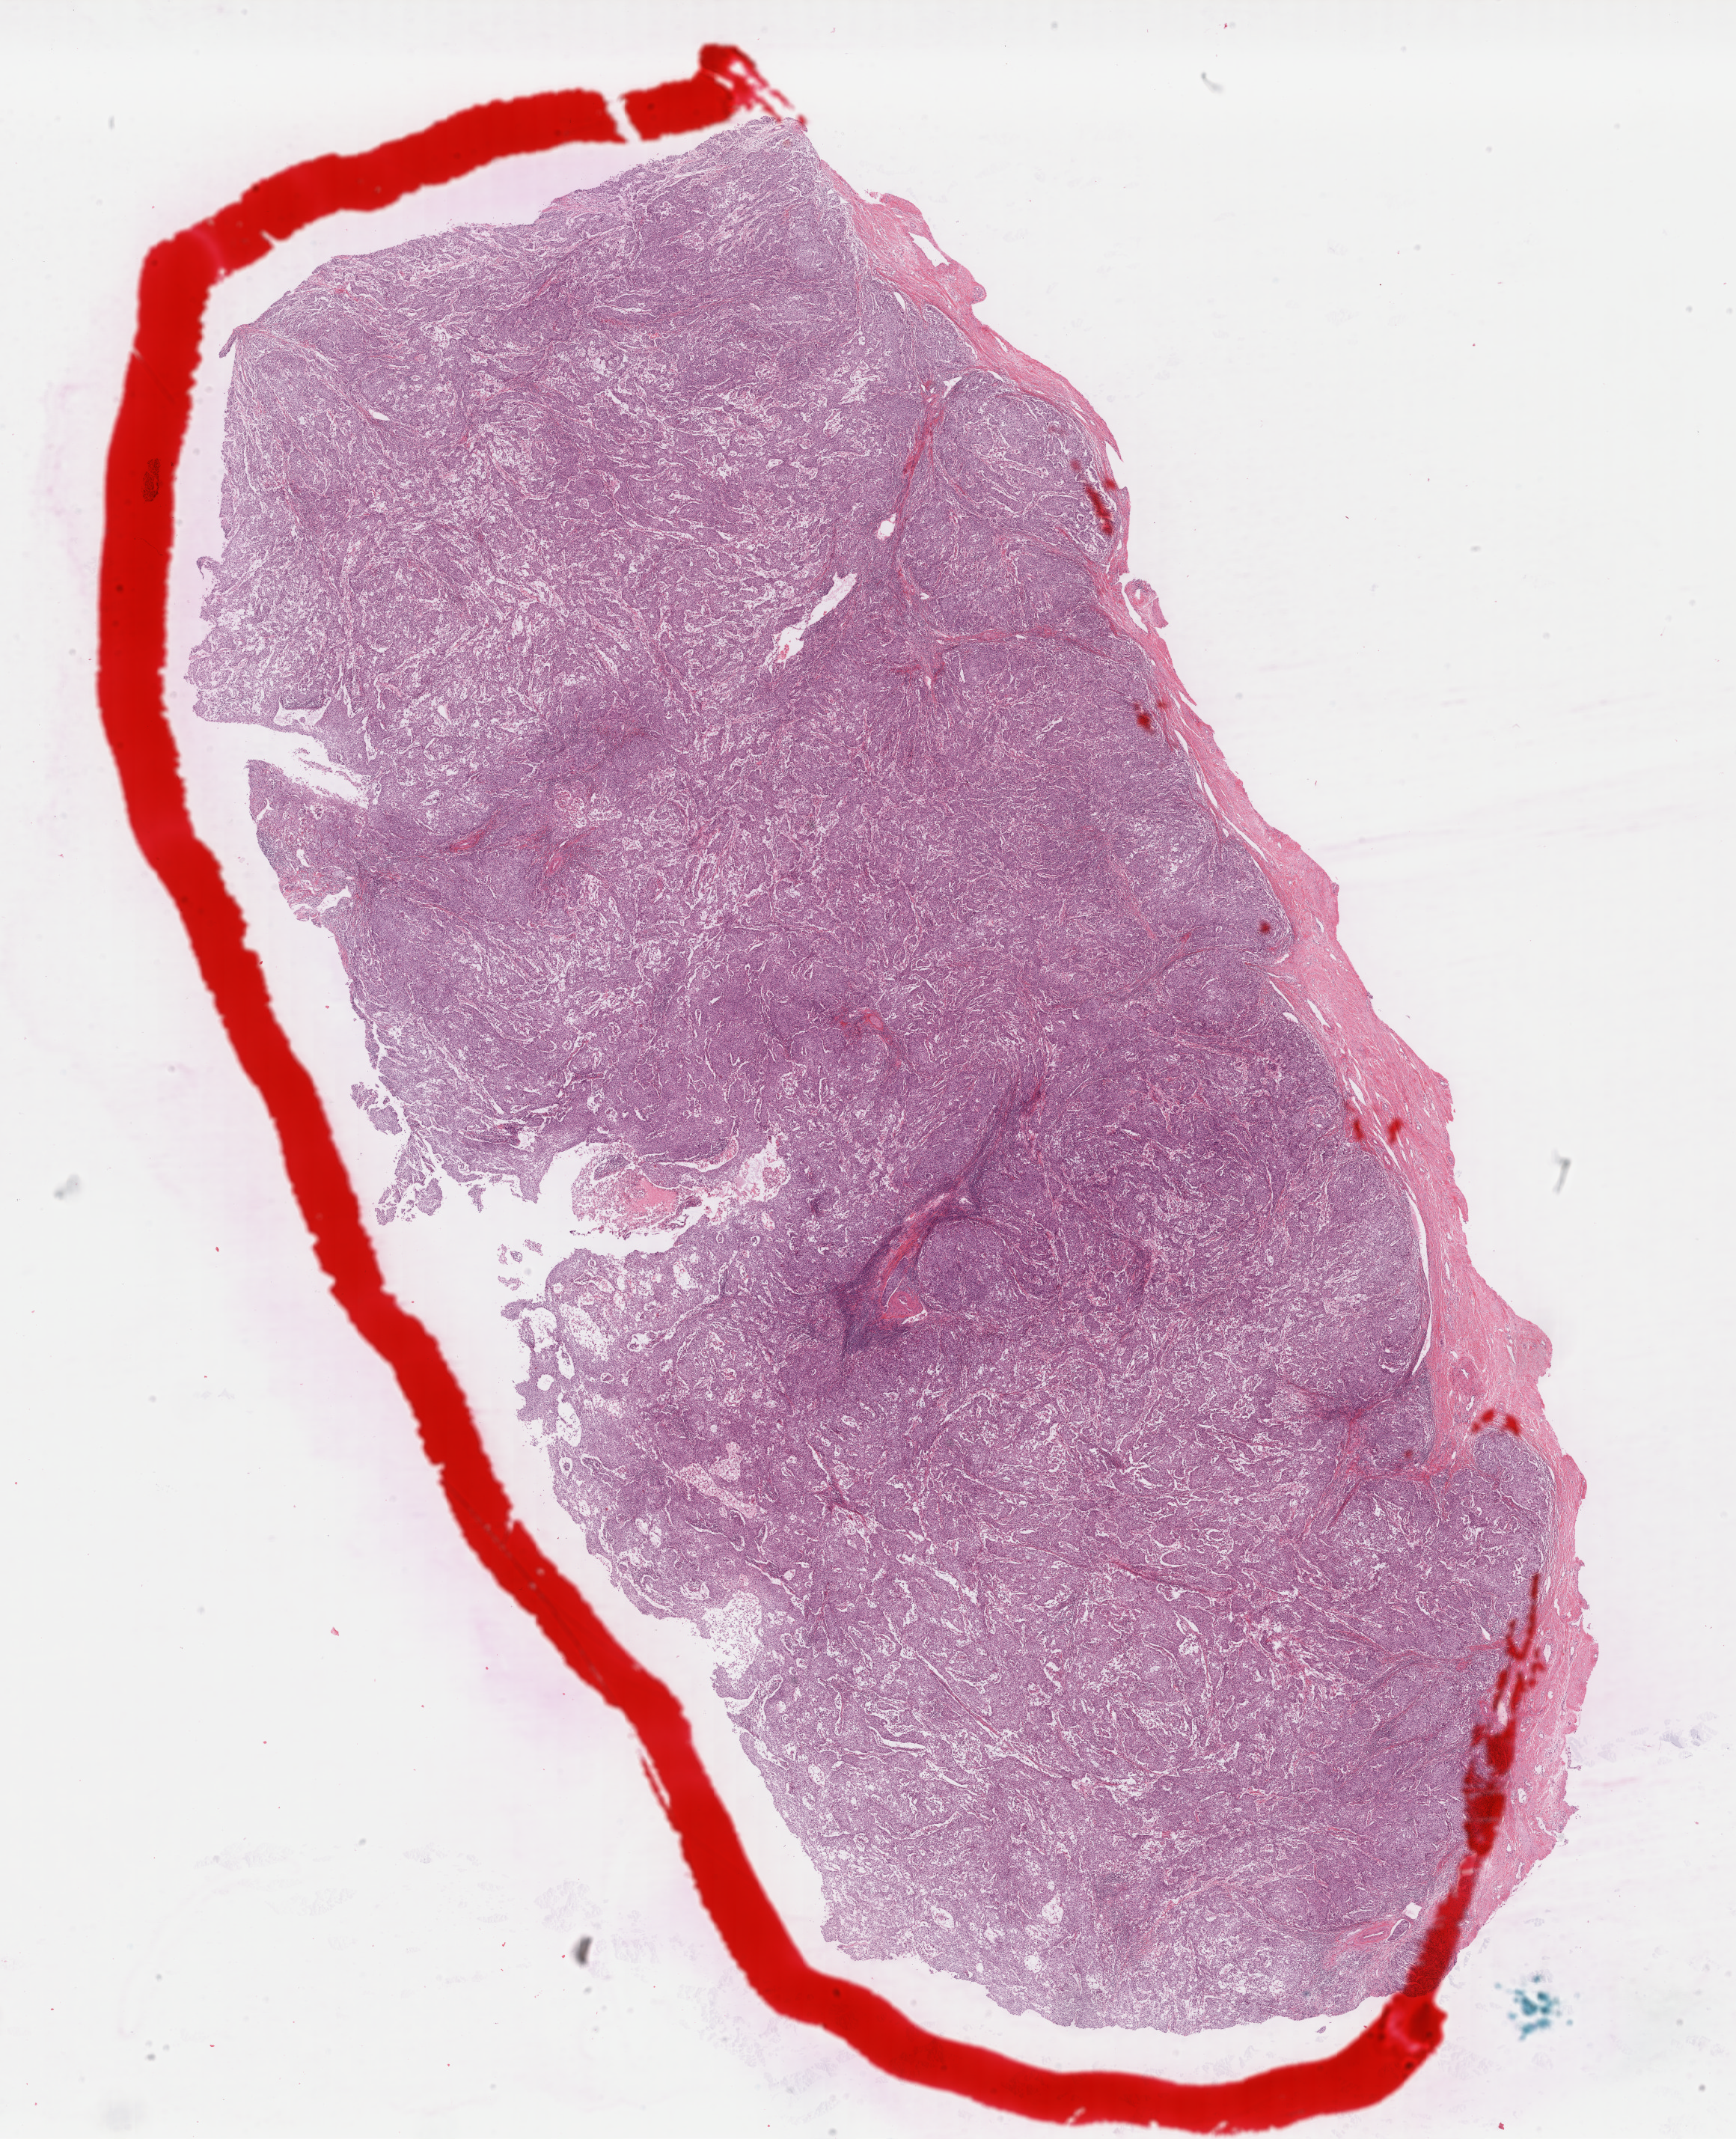
Digitized Hematoxylin and eosin (H&E) stained tissue section (whole slide) — a low-resolution overview of the entire scanned area, about 18.4 x 22.7 mm (slide scanned at 40x); formalin-fixed paraffin-embedded (FFPE) diagnostic section; primary tumour sample from the cervix. Female, age 43 years at initial diagnosis. Histologic grade: G2 (moderately differentiated).
FIGO stage: II. Pathologic diagnosis: Squamous cell carcinoma, NOS.